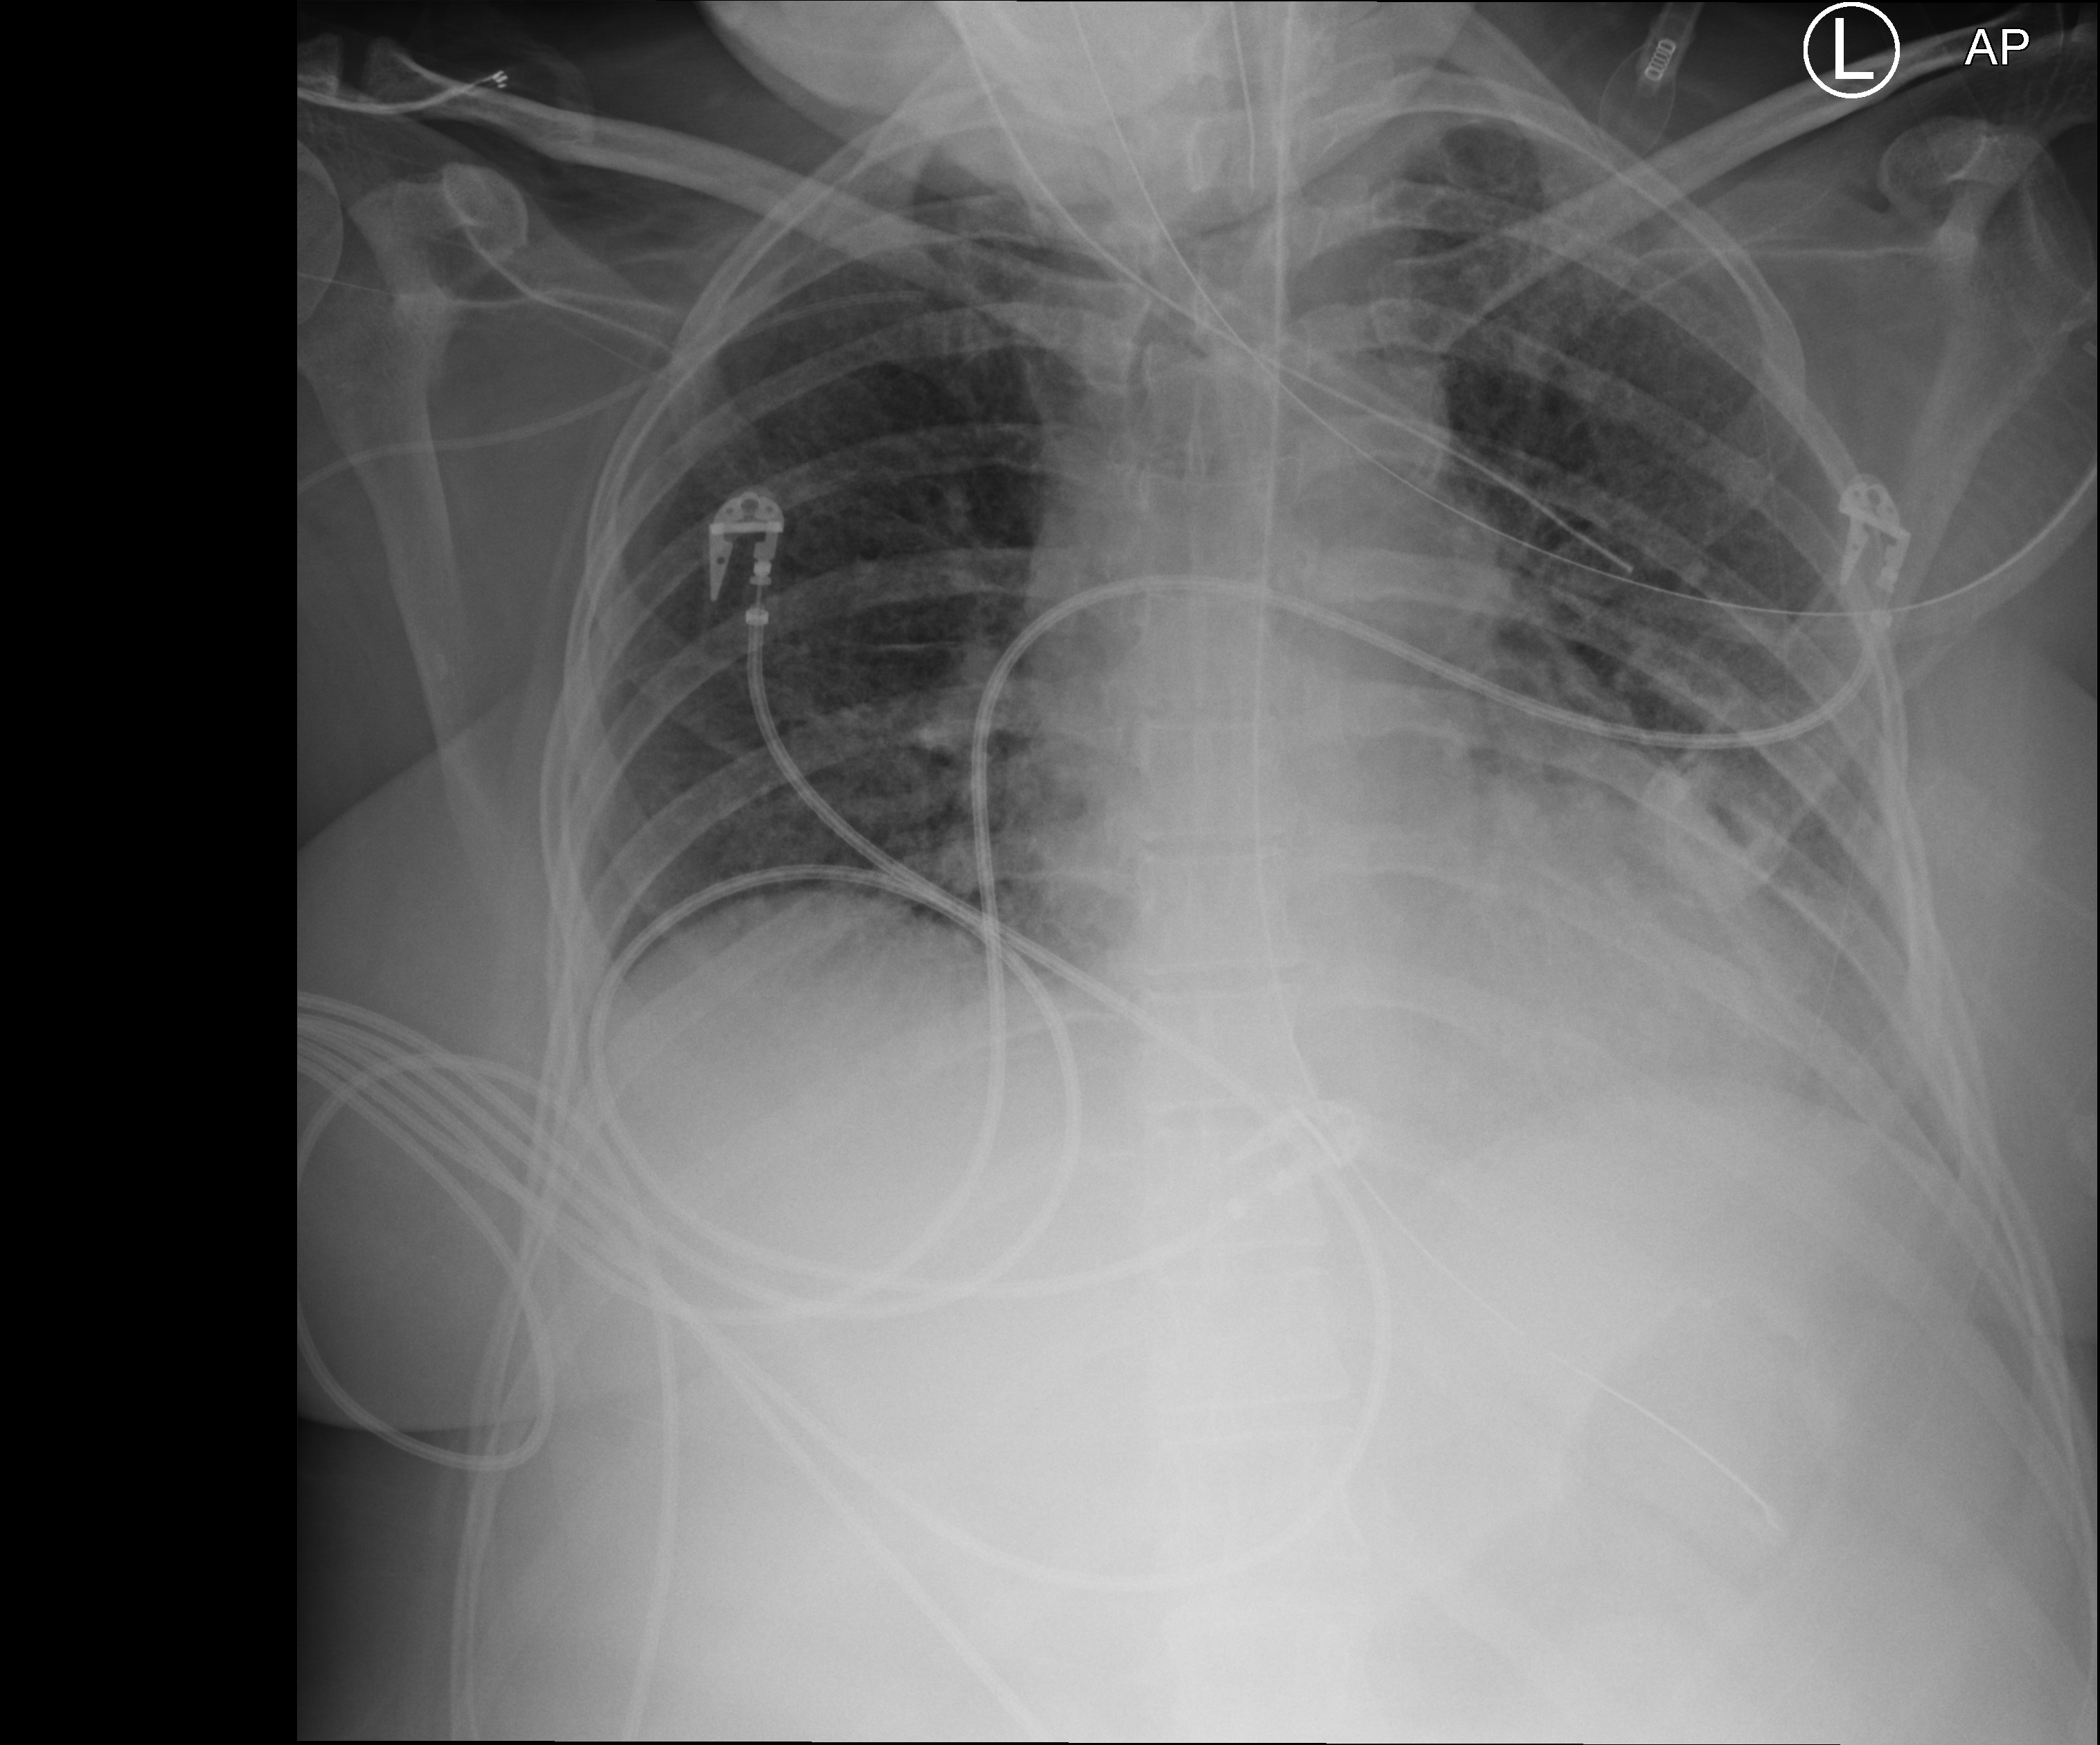
Chest X-ray (portable); anteroposterior (AP) projection. Patient hospitalised with COVID-19; female, aged 18–59 years.
Hospital-stay facts (about this admission, not read from this image; timing relative to this image not recorded): mechanically ventilated during this hospital stay: yes.